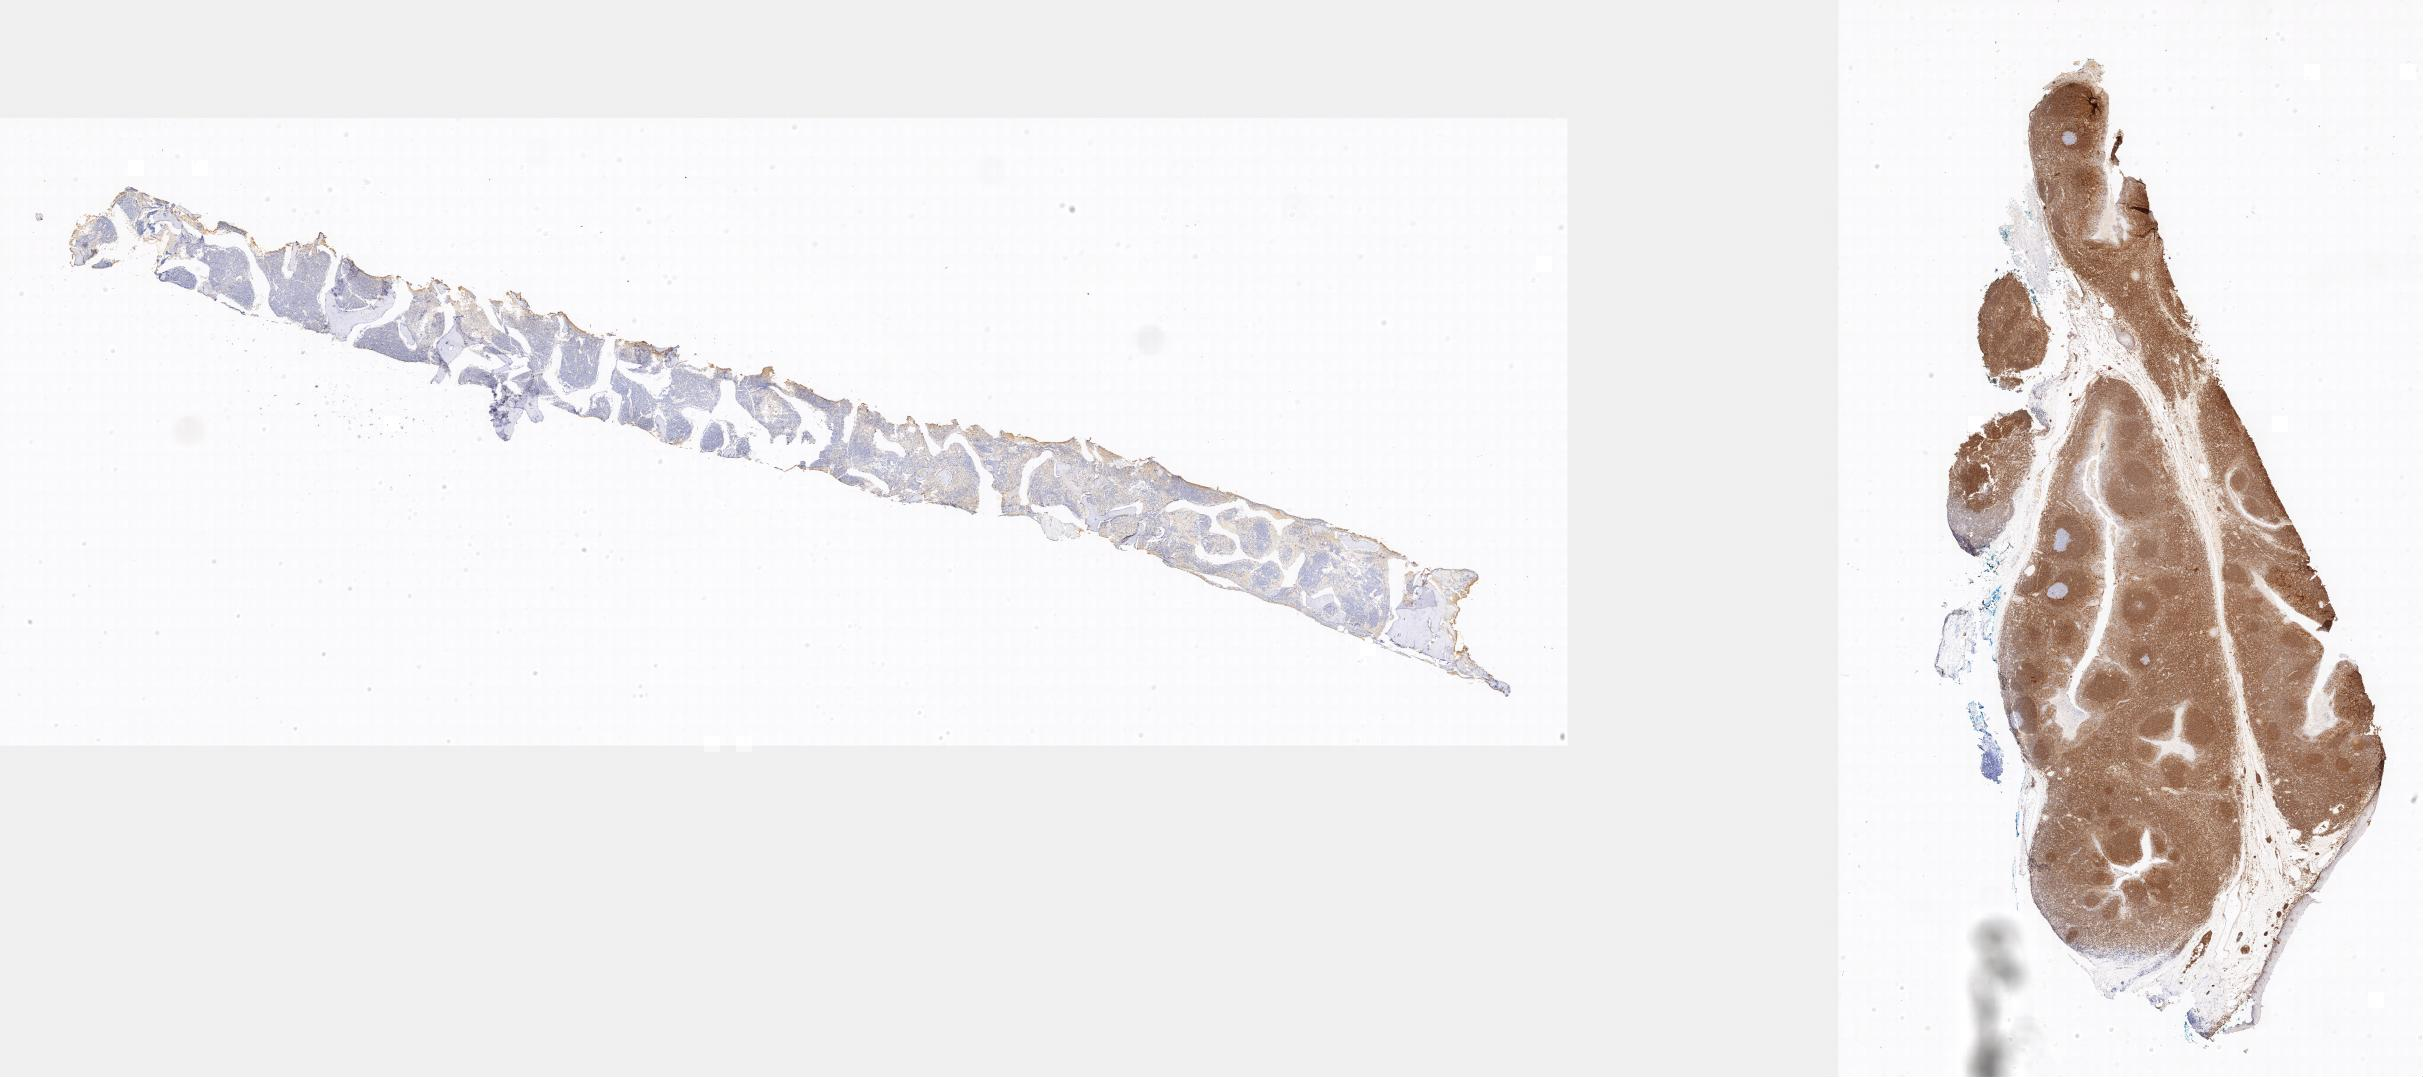
Whole-slide image, immunohistochemical stain for BCL2, a low-resolution overview of the entire scanned area. Tumor tissue. Site: bone marrow. Patient male; 18 years old.
Diagnosis: Burkitt lymphoma, NOS.